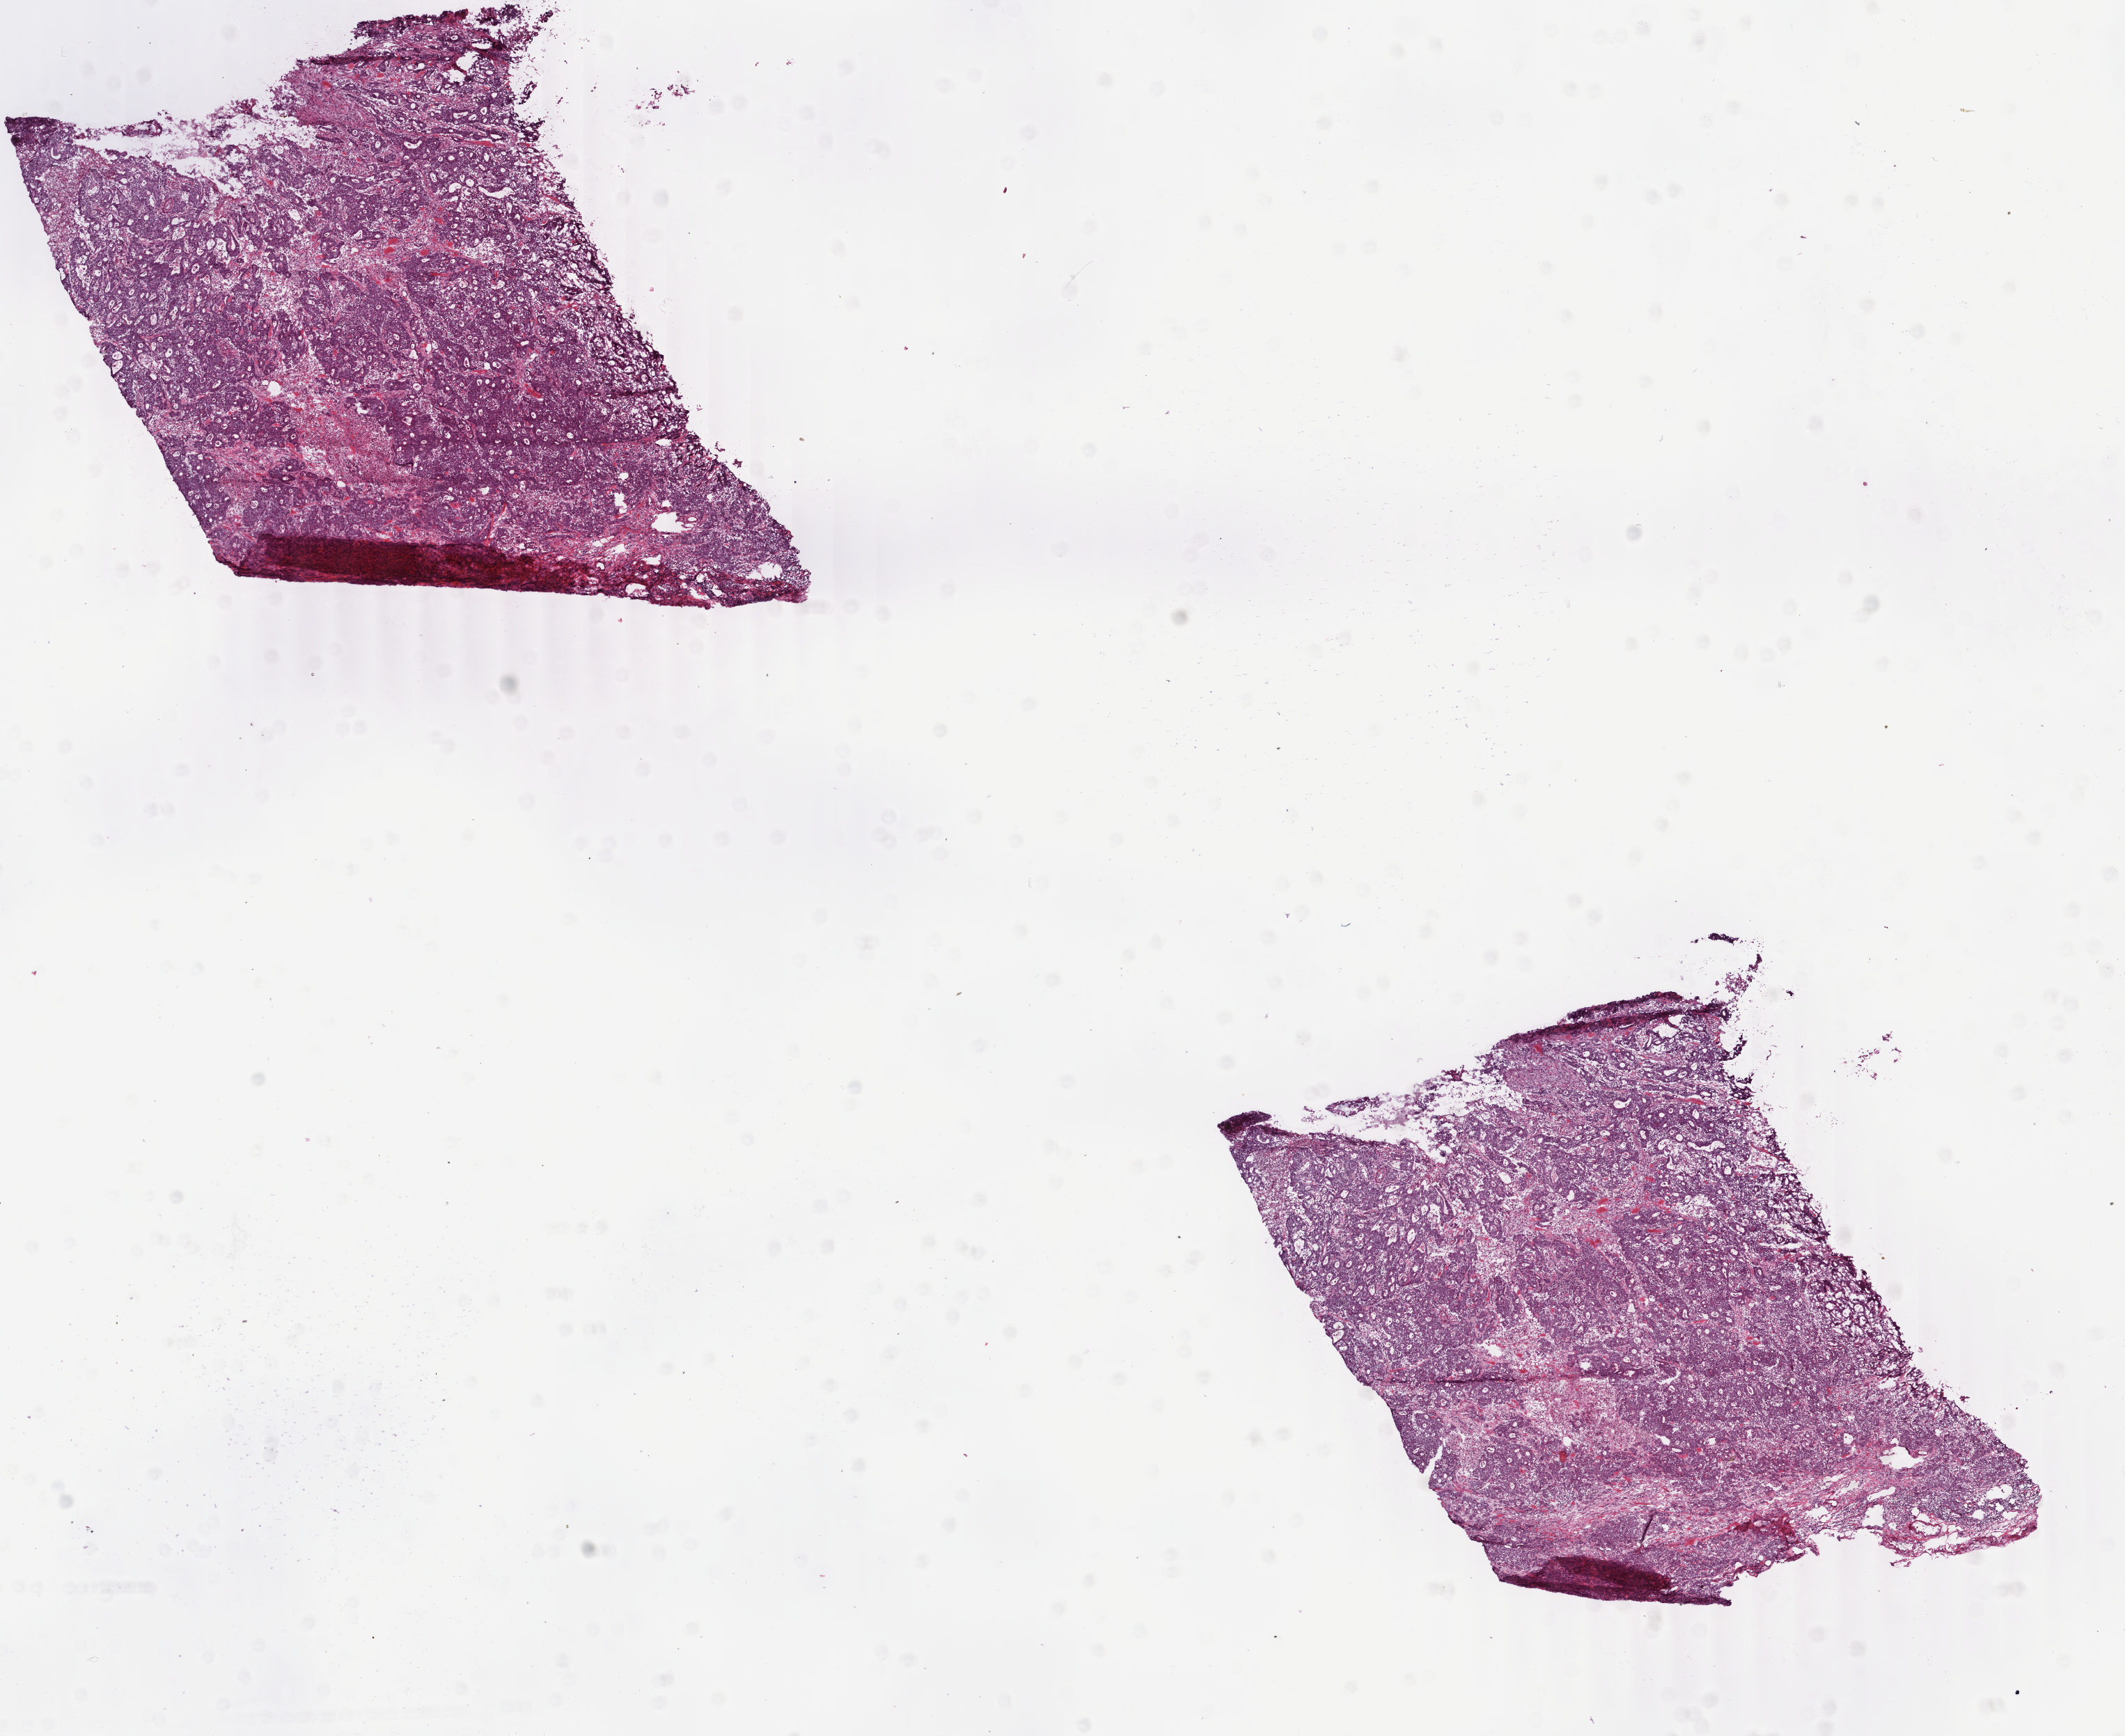
Whole-slide histology image, Hematoxylin and eosin (H&E) stained, low-resolution overview of the scanned area, about 12.1 x 9.9 mm (slide scanned at 40x); frozen section; primary tumour sample from the colon. Patient: male, age at initial diagnosis 47 years. Slide review estimates, as recorded: tumour cells 85%, tumour nuclei 85%, normal cells 0%, stromal cells 12%, necrosis 3%. Infiltration values recorded for this section: lymphocyte infiltration 5%, monocyte infiltration 2%, neutrophil infiltration 5%.
- AJCC pathologic stage: III (5th edition)
- pathologic diagnosis: Mucinous adenocarcinoma (ascending colon)
- TNM: T3 N2 M0